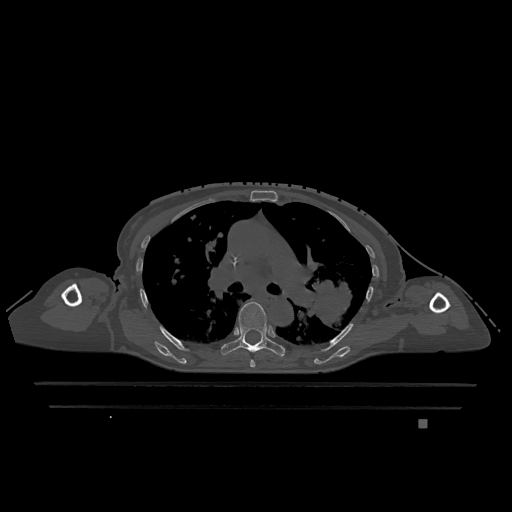
CT including the spine, one axial slice. Slice 797 of 1317 in the series (ordered by position). Bone window (W 1800 / L 400 HU). 0.5 mm slice thickness. 512 × 512 image matrix. Female patient, age 74 years. Case-level facts recorded for this patient, not image findings: primary cancer: lung; vertebrae with lytic lesions (as recorded): T1, T4, T5, T6, L4, L5.
Annotated regions visible in this slice (semi-automatic segmentation, software-assisted and operator-edited):
- T5 vertebra: bounding box [x1, y1, x2, y2] px = [250, 360, 256, 368]
- T6 vertebra: [221, 302, 285, 357]